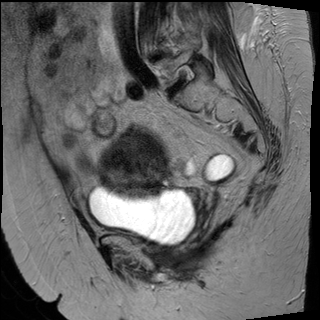
Pelvic MRI for cervical cancer, one sagittal slice; slice 30 of 50 in the series (ordered by position); T2-weighted; 1.5 T; TE 89 ms, TR 4880 ms; 4 mm slice thickness; 320 × 320 image matrix. Patient: female, 50 years.
Structures marked on this image (outlined manually by an expert reader):
- uterus and cervix: box from (x=96, y=130) to (x=171, y=202) px